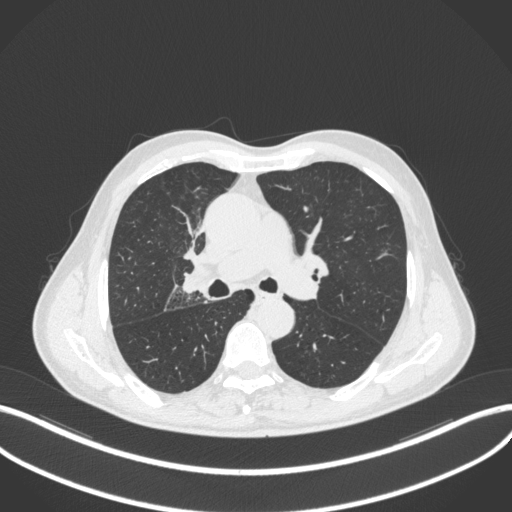
Chest CT, one axial slice; reconstruction kernel B31f; 120 kVp; lung window (W 1500 / L -600 HU); 1 mm slice thickness; 512 × 512 image matrix, field of view 400 × 400 mm. Male patient, age 69 years. From the clinical record (not read from this slice): clinical TNM (as recorded): T2a N0 M0.
Structures marked on this image (rectangle marked by the reading radiologist):
- lung tumour (recorded histology: adenocarcinoma): box from (x=182, y=261) to (x=212, y=293) px